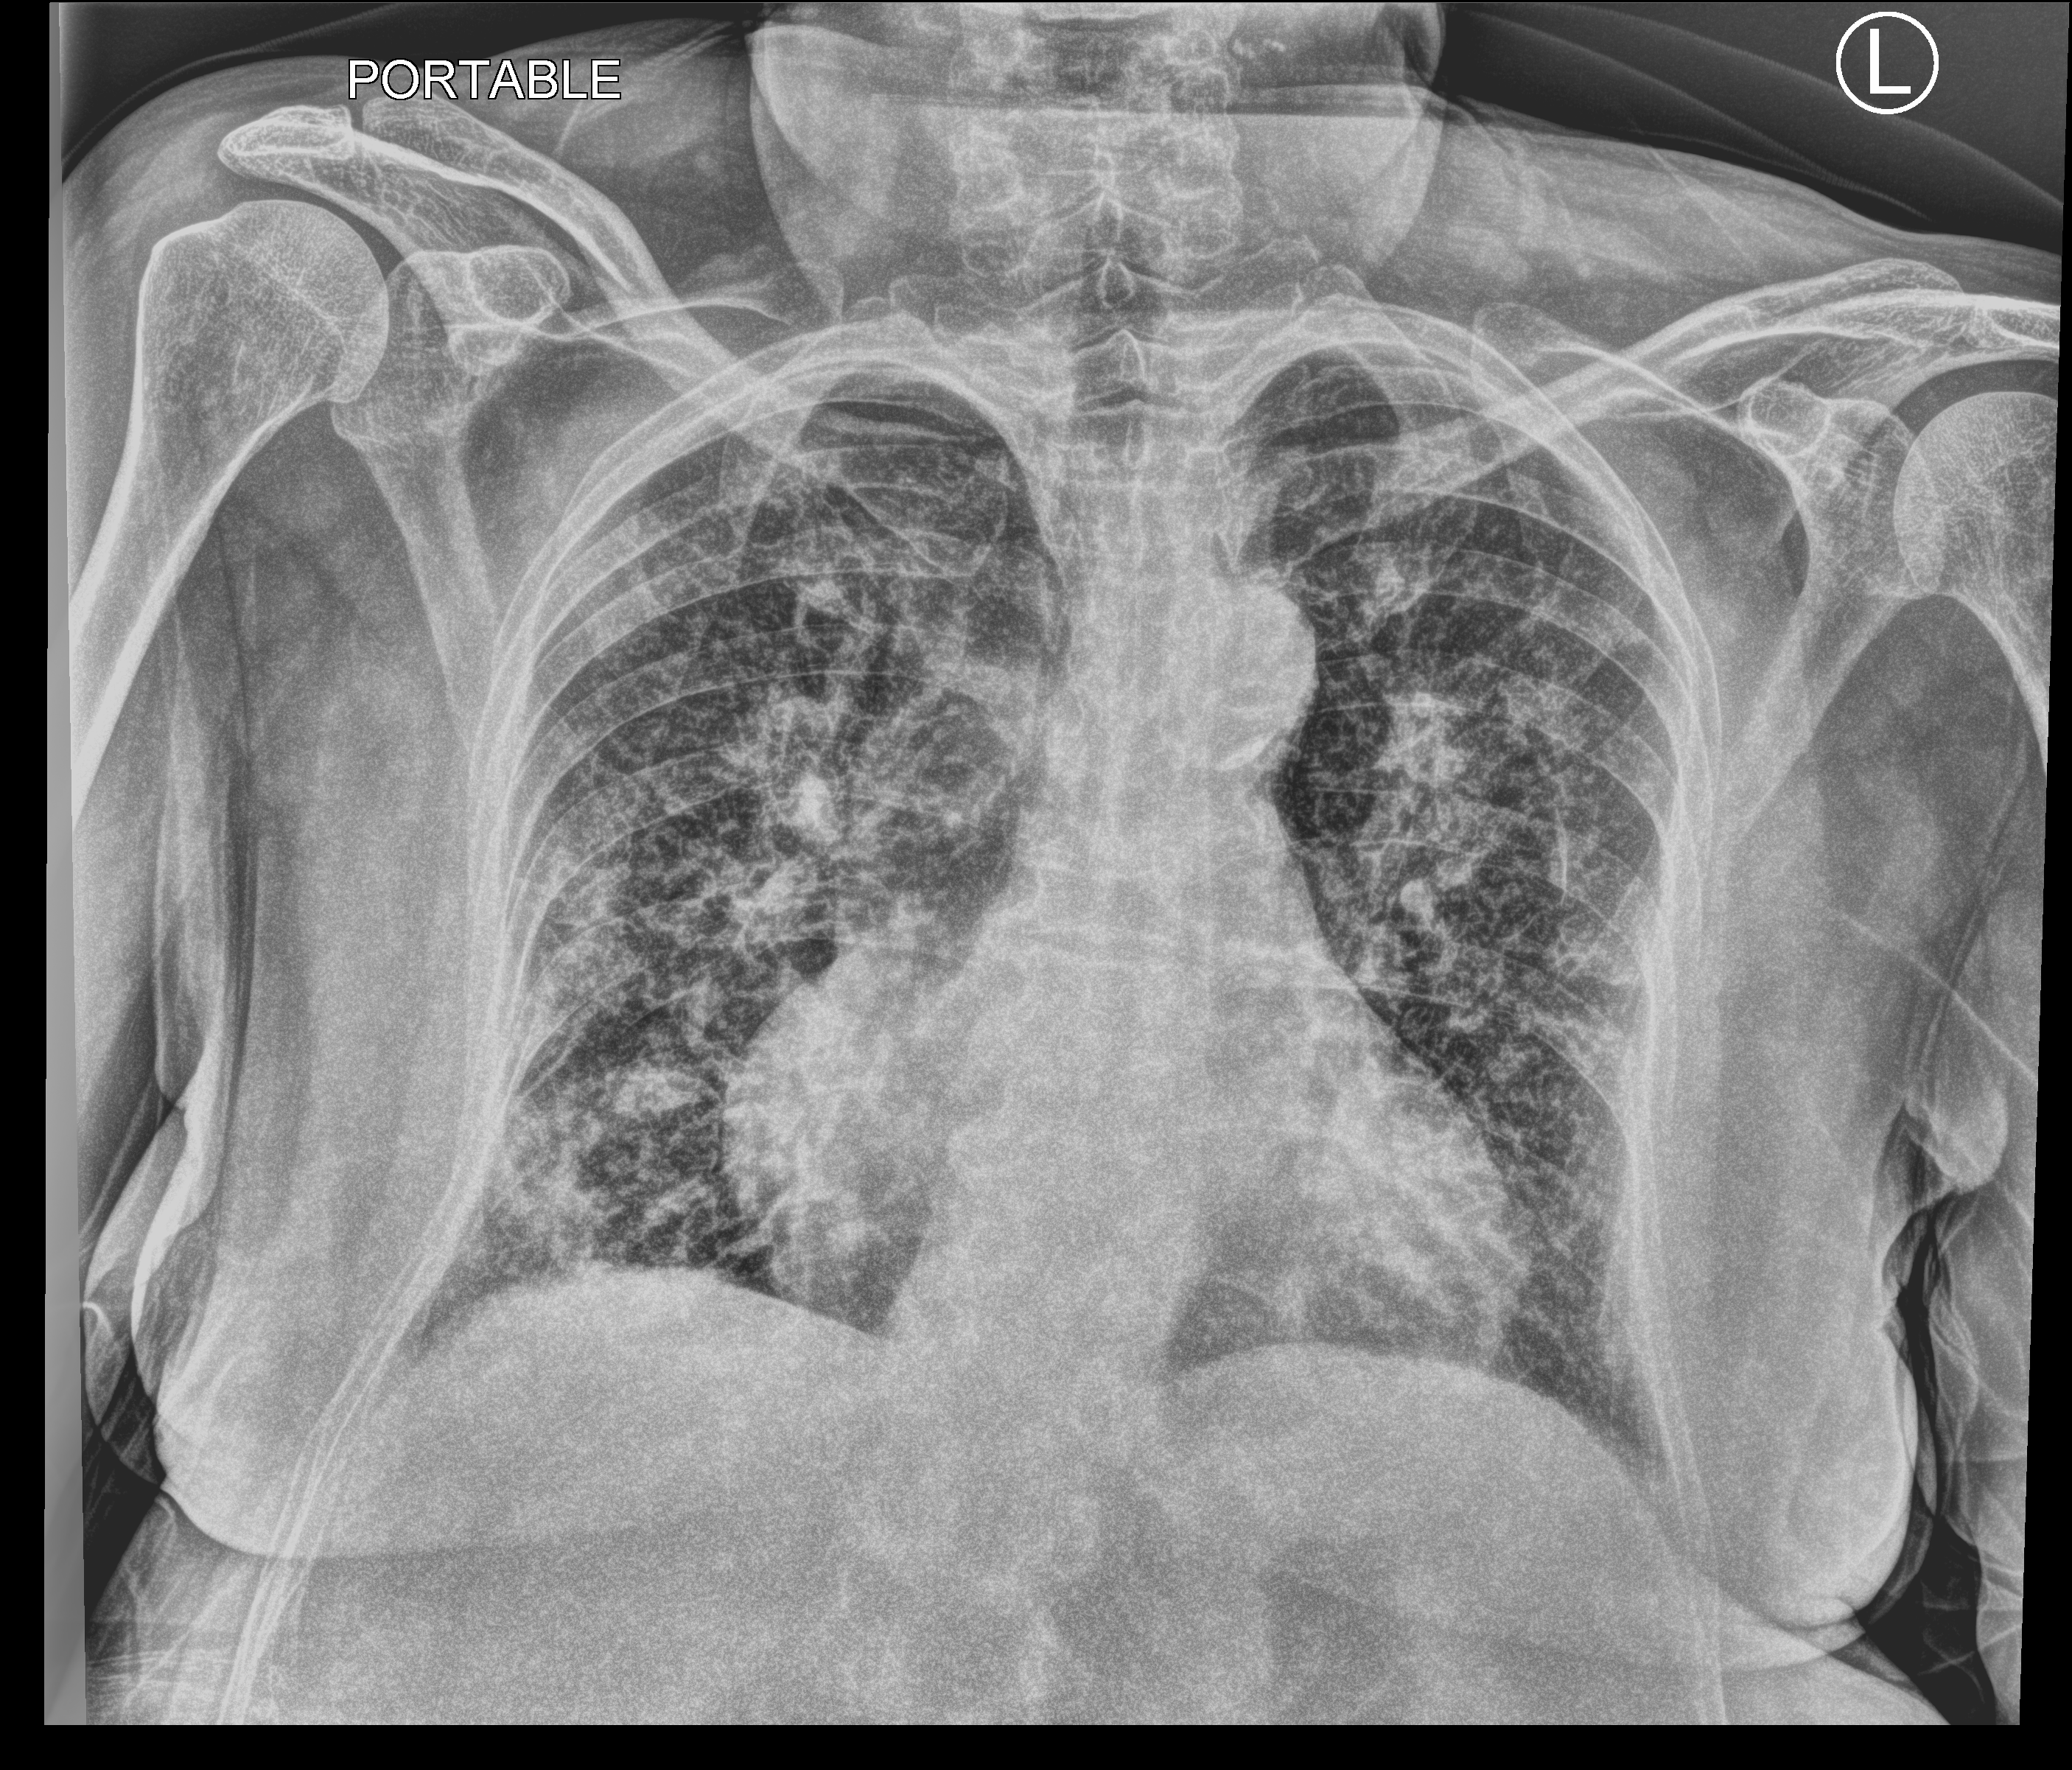
Portable chest radiograph, anteroposterior (AP) projection. Female patient hospitalised with COVID-19, age 75–90 years.
From the hospital-stay record, not from the radiograph (when in the stay this image was taken is not recorded):
- admitted to intensive care during this hospital stay: yes
- mechanically ventilated during this hospital stay: yes